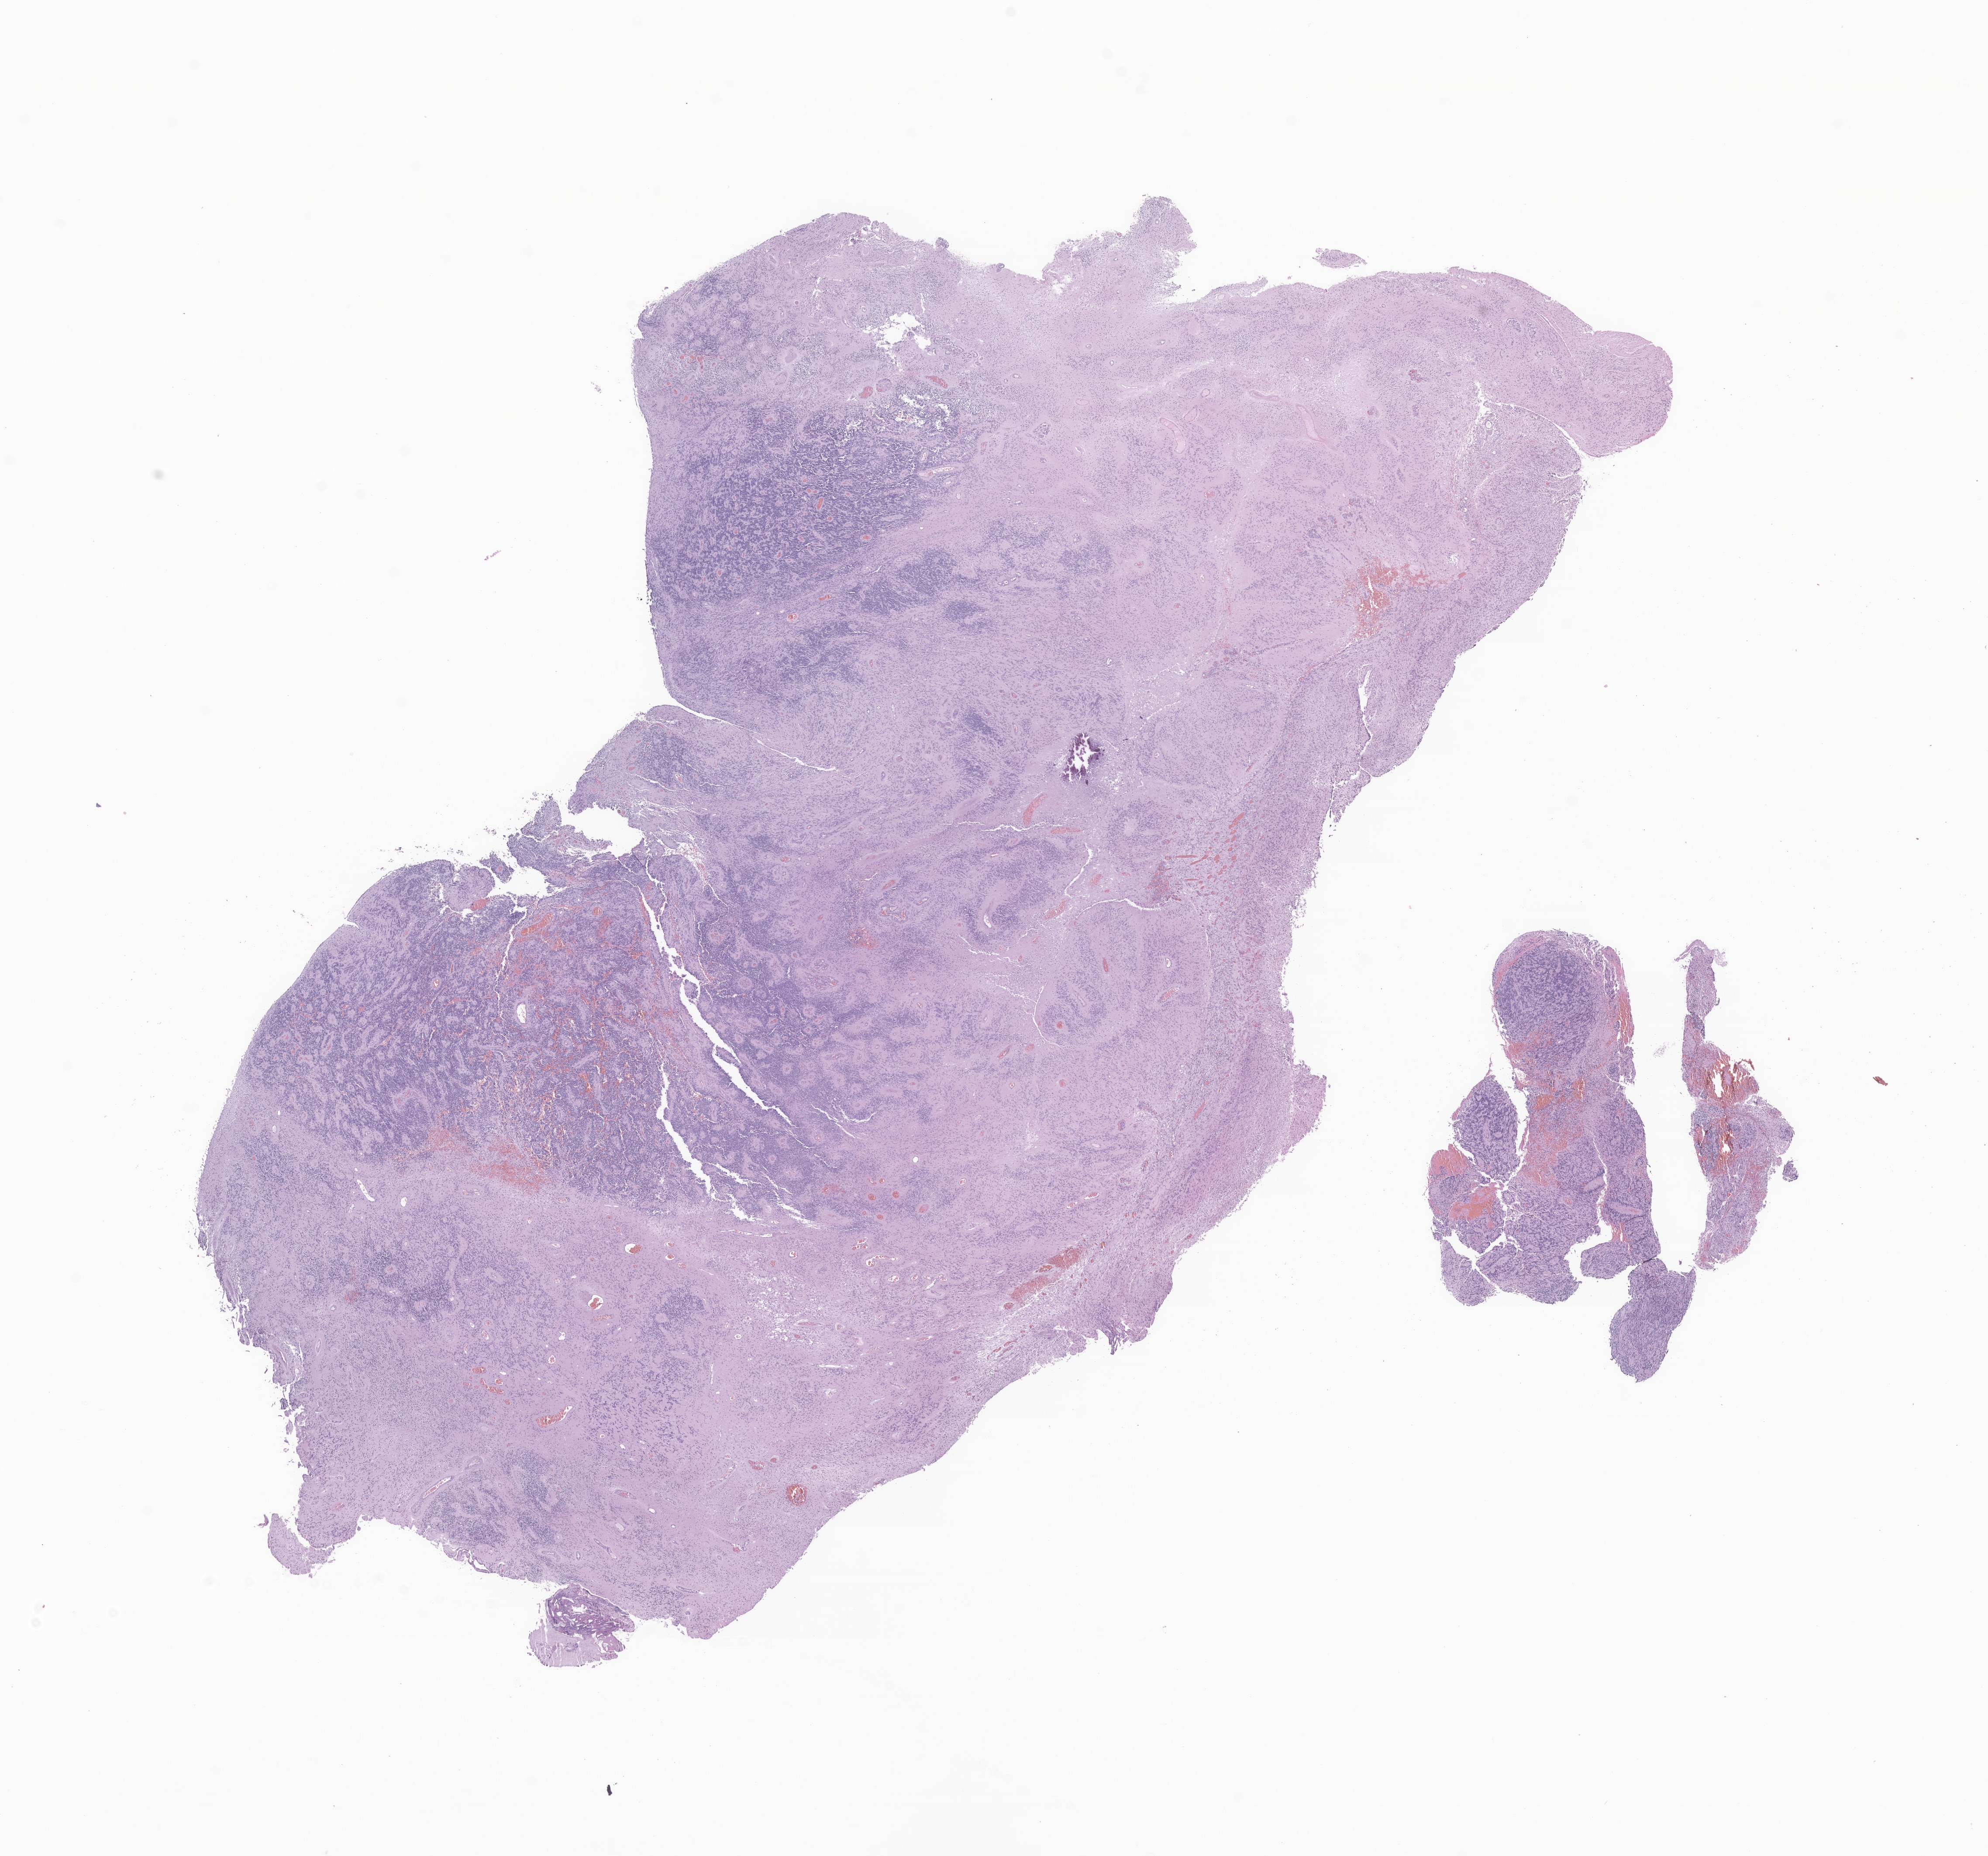
Whole-slide image, hematoxylin and eosin (H&E) stain of tumor tissue from the brain — low-resolution overview of the scanned area, about 19.2 x 17.9 mm. Formalin-fixed, paraffin-embedded (FFPE) tissue. Patient female; age 73 months (6 years 1 month).
• diagnosis (ICD-O-3 morphology term): Neoplasm, uncertain whether benign or malignant